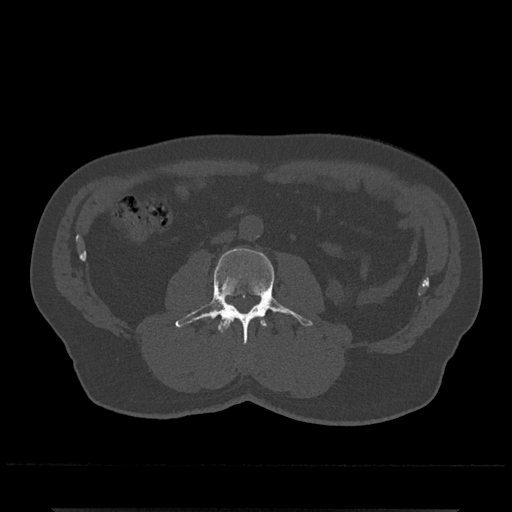
CT including the spine, one axial slice. Slice 225 of 797 in the series (ordered by position). Bone window (W 1800 / L 400 HU). 512 × 512 image matrix, field of view 393 × 393 mm. Male patient, age 67 years. Case-level facts recorded for this patient, not image findings: primary cancer: prostate.
Outlined on this slice (semi-automatically segmented with operator editing):
- L2 vertebra: bounding box [x1, y1, x2, y2] px = [219, 318, 266, 333]
- L3 vertebra: [175, 248, 313, 344]